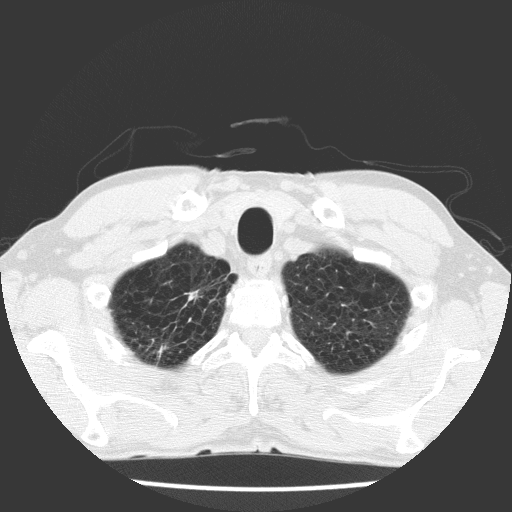
Axial slice from a low-dose chest CT screening exam. First (baseline) screen. Lung window (W 1500 / L -600 HU). Slice 14 of 172 in the series. 512 × 512 image matrix, field of view 325 × 325 mm. Male, age 63 years at enrolment.
Expert reader's lesion annotation, bounding box <160,279,218,335> (left, top, right, bottom; pixels). No non-calcified nodule or mass ≥4 mm was recorded by the screening reader at this exam. Official screen result: negative screen, significant abnormalities not suspicious for lung cancer. Lung cancer was diagnosed 741 days after this screen: adenocarcinoma, NOS, right upper lobe, moderately differentiated (G2), stage IIIB (AJCC 6th edition), 17 mm at pathology.